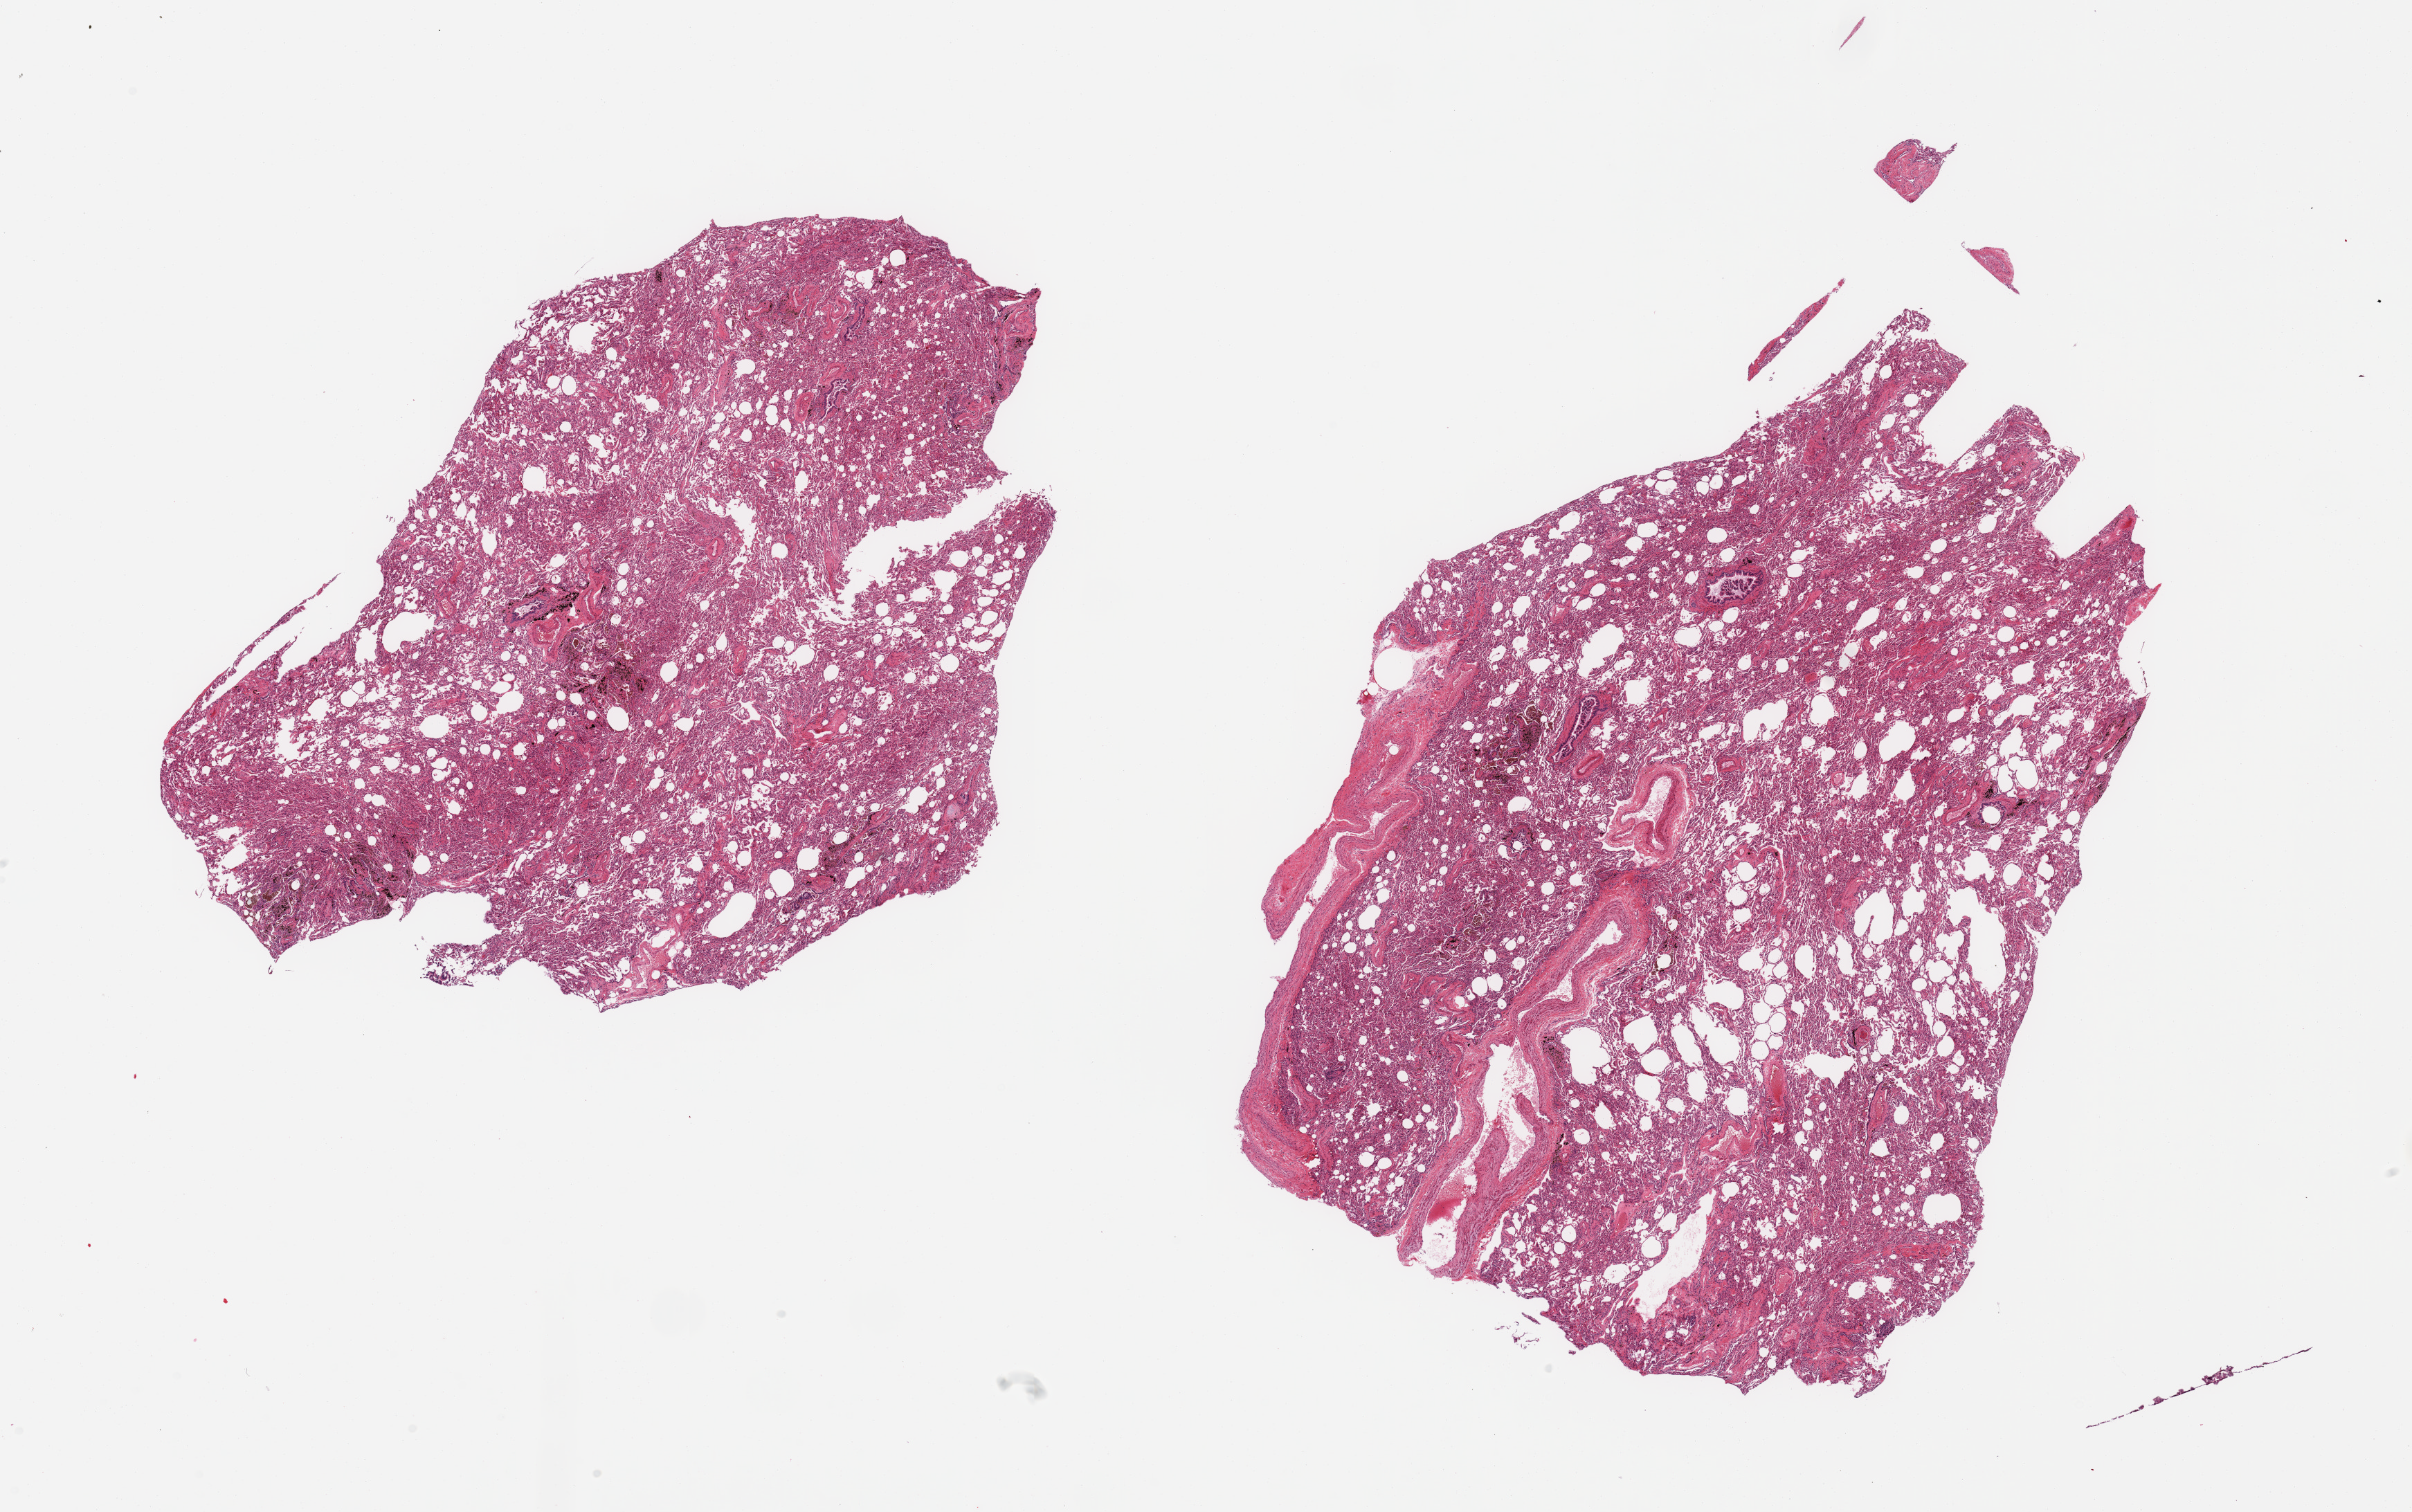
Hematoxylin and eosin (H&E) whole-slide image — shown as a low-resolution overview of the whole scanned area (about 27.6 x 17.3 mm, acquisition: 20x scan), PAXgene-fixed, paraffin-embedded tissue, section of lung (target tissue), donor tissue sample. Donor sex: female.
* review note (as recorded): 2 pieces; no fibrosis; focal alveolar, bronchial and peribronchial collections of pigmented macrophages